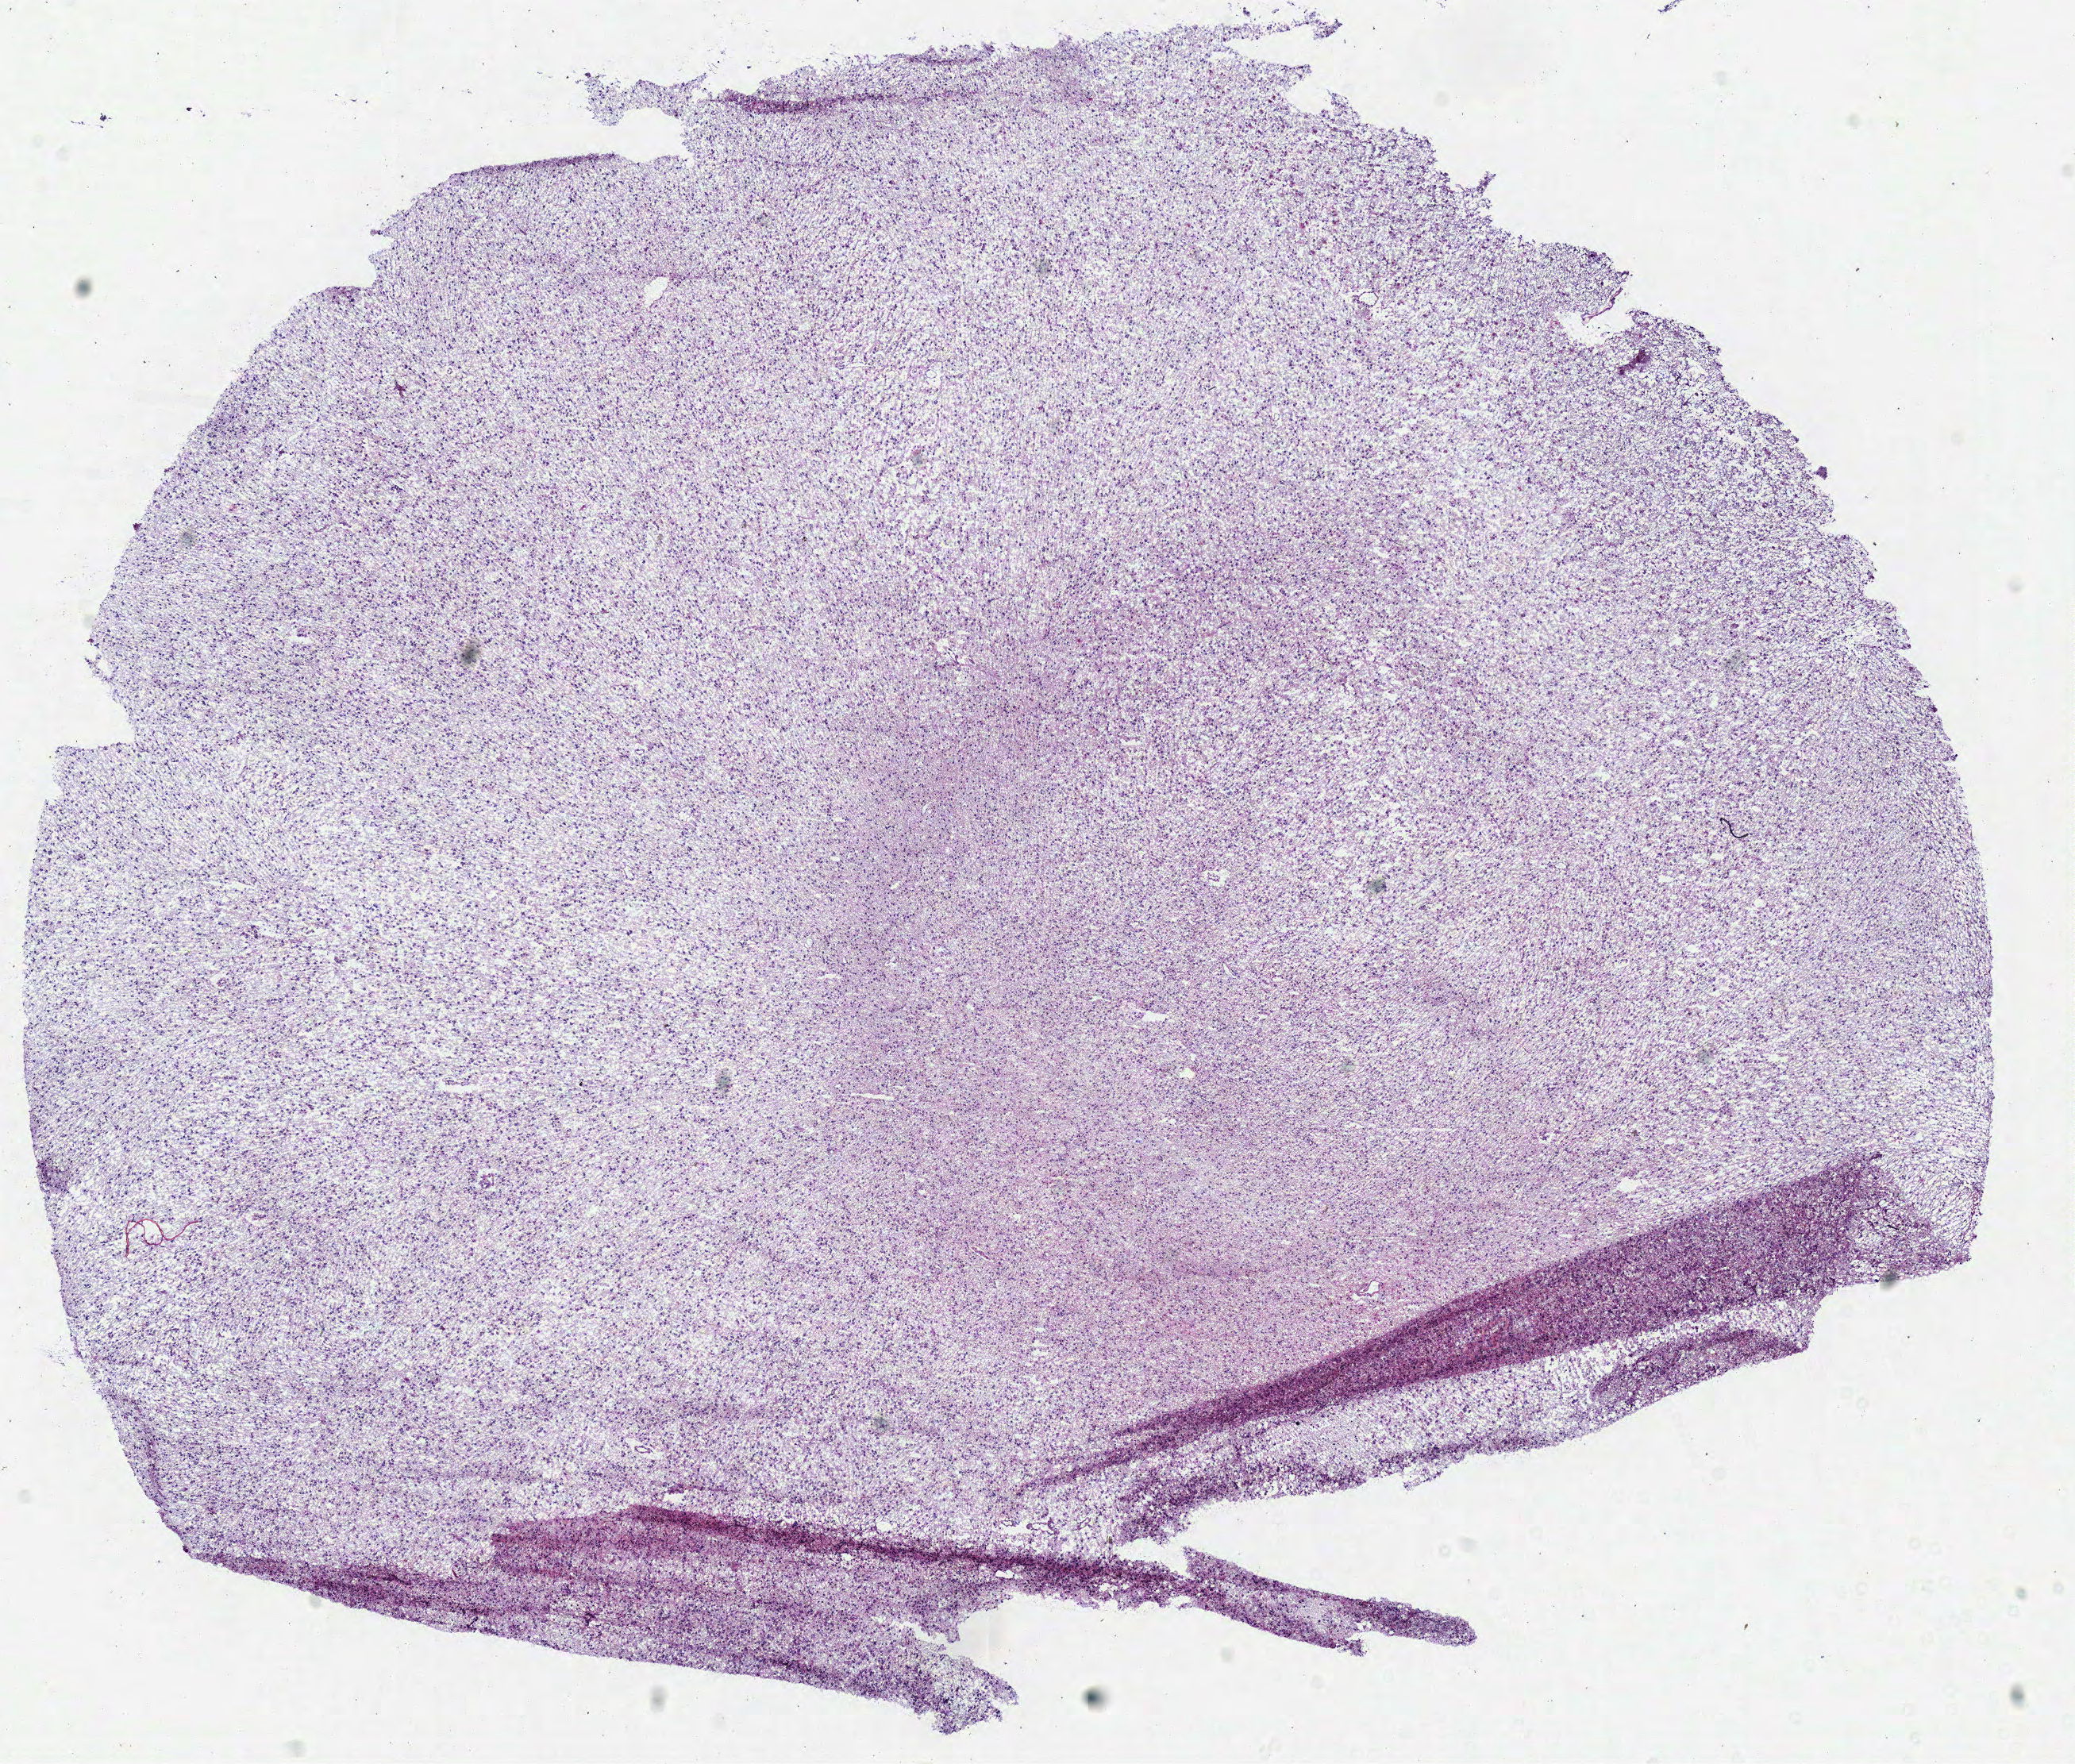
Digitized H&E-stained tissue section (whole slide) — low-resolution overview of the scanned area, about 10.3 x 8.7 mm (slide scanned at 40x); frozen section from the bottom of the tissue portion; sample: primary tumour, brain. Patient: male, age at initial diagnosis 60 years. Composition of this section per pathologist review: tumour cells 100%, tumour nuclei 75%, normal cells 0%, stromal cells 0%, necrosis 0%.
• diagnosis: Glioblastoma